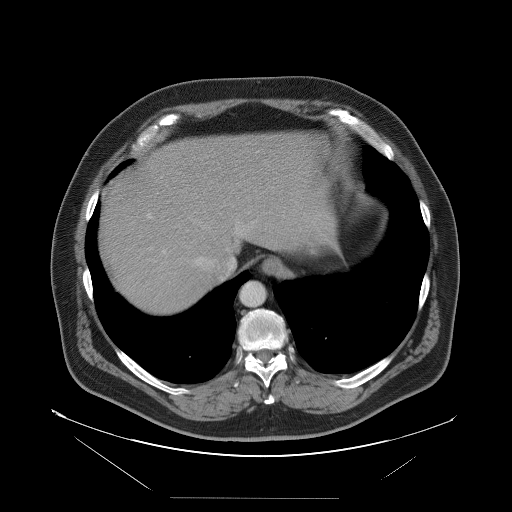
Contrast-enhanced abdominal CT, one axial slice; position 84 of 114 along the scan axis; soft-tissue window (W 400 / L 40 HU); 5 mm slice thickness; 512 × 512 image matrix, field of view 500 × 500 mm. Male patient, age 61 years. From the clinical record (not read from this slice): diagnosis: colorectal cancer liver metastases, imaged before liver resection; multiple liver metastases: no; largest metastasis: 6.5 cm.
Structures marked on this image (manually delineated by an expert):
- hepatic veins: bounding box <181,215,257,275> (left, top, right, bottom; pixels)
- liver: <97,132,318,318>
- planned liver remnant (the part of the liver to remain after resection): <151,131,318,282>